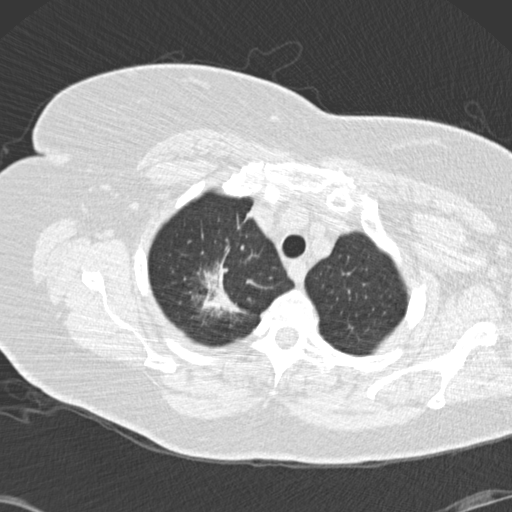
Low-dose screening chest CT, one axial slice. Slice 124 of 146 in the series (ordered by position). Lung window (W 1500 / L -600 HU). 2 mm slice thickness. 512 × 512 image matrix, field of view 350 × 350 mm.
Structures marked on this image (outlined manually by an expert reader):
- lesion 1 (tumor, upper lobe of right lung): box from (x=201, y=262) to (x=244, y=316) px